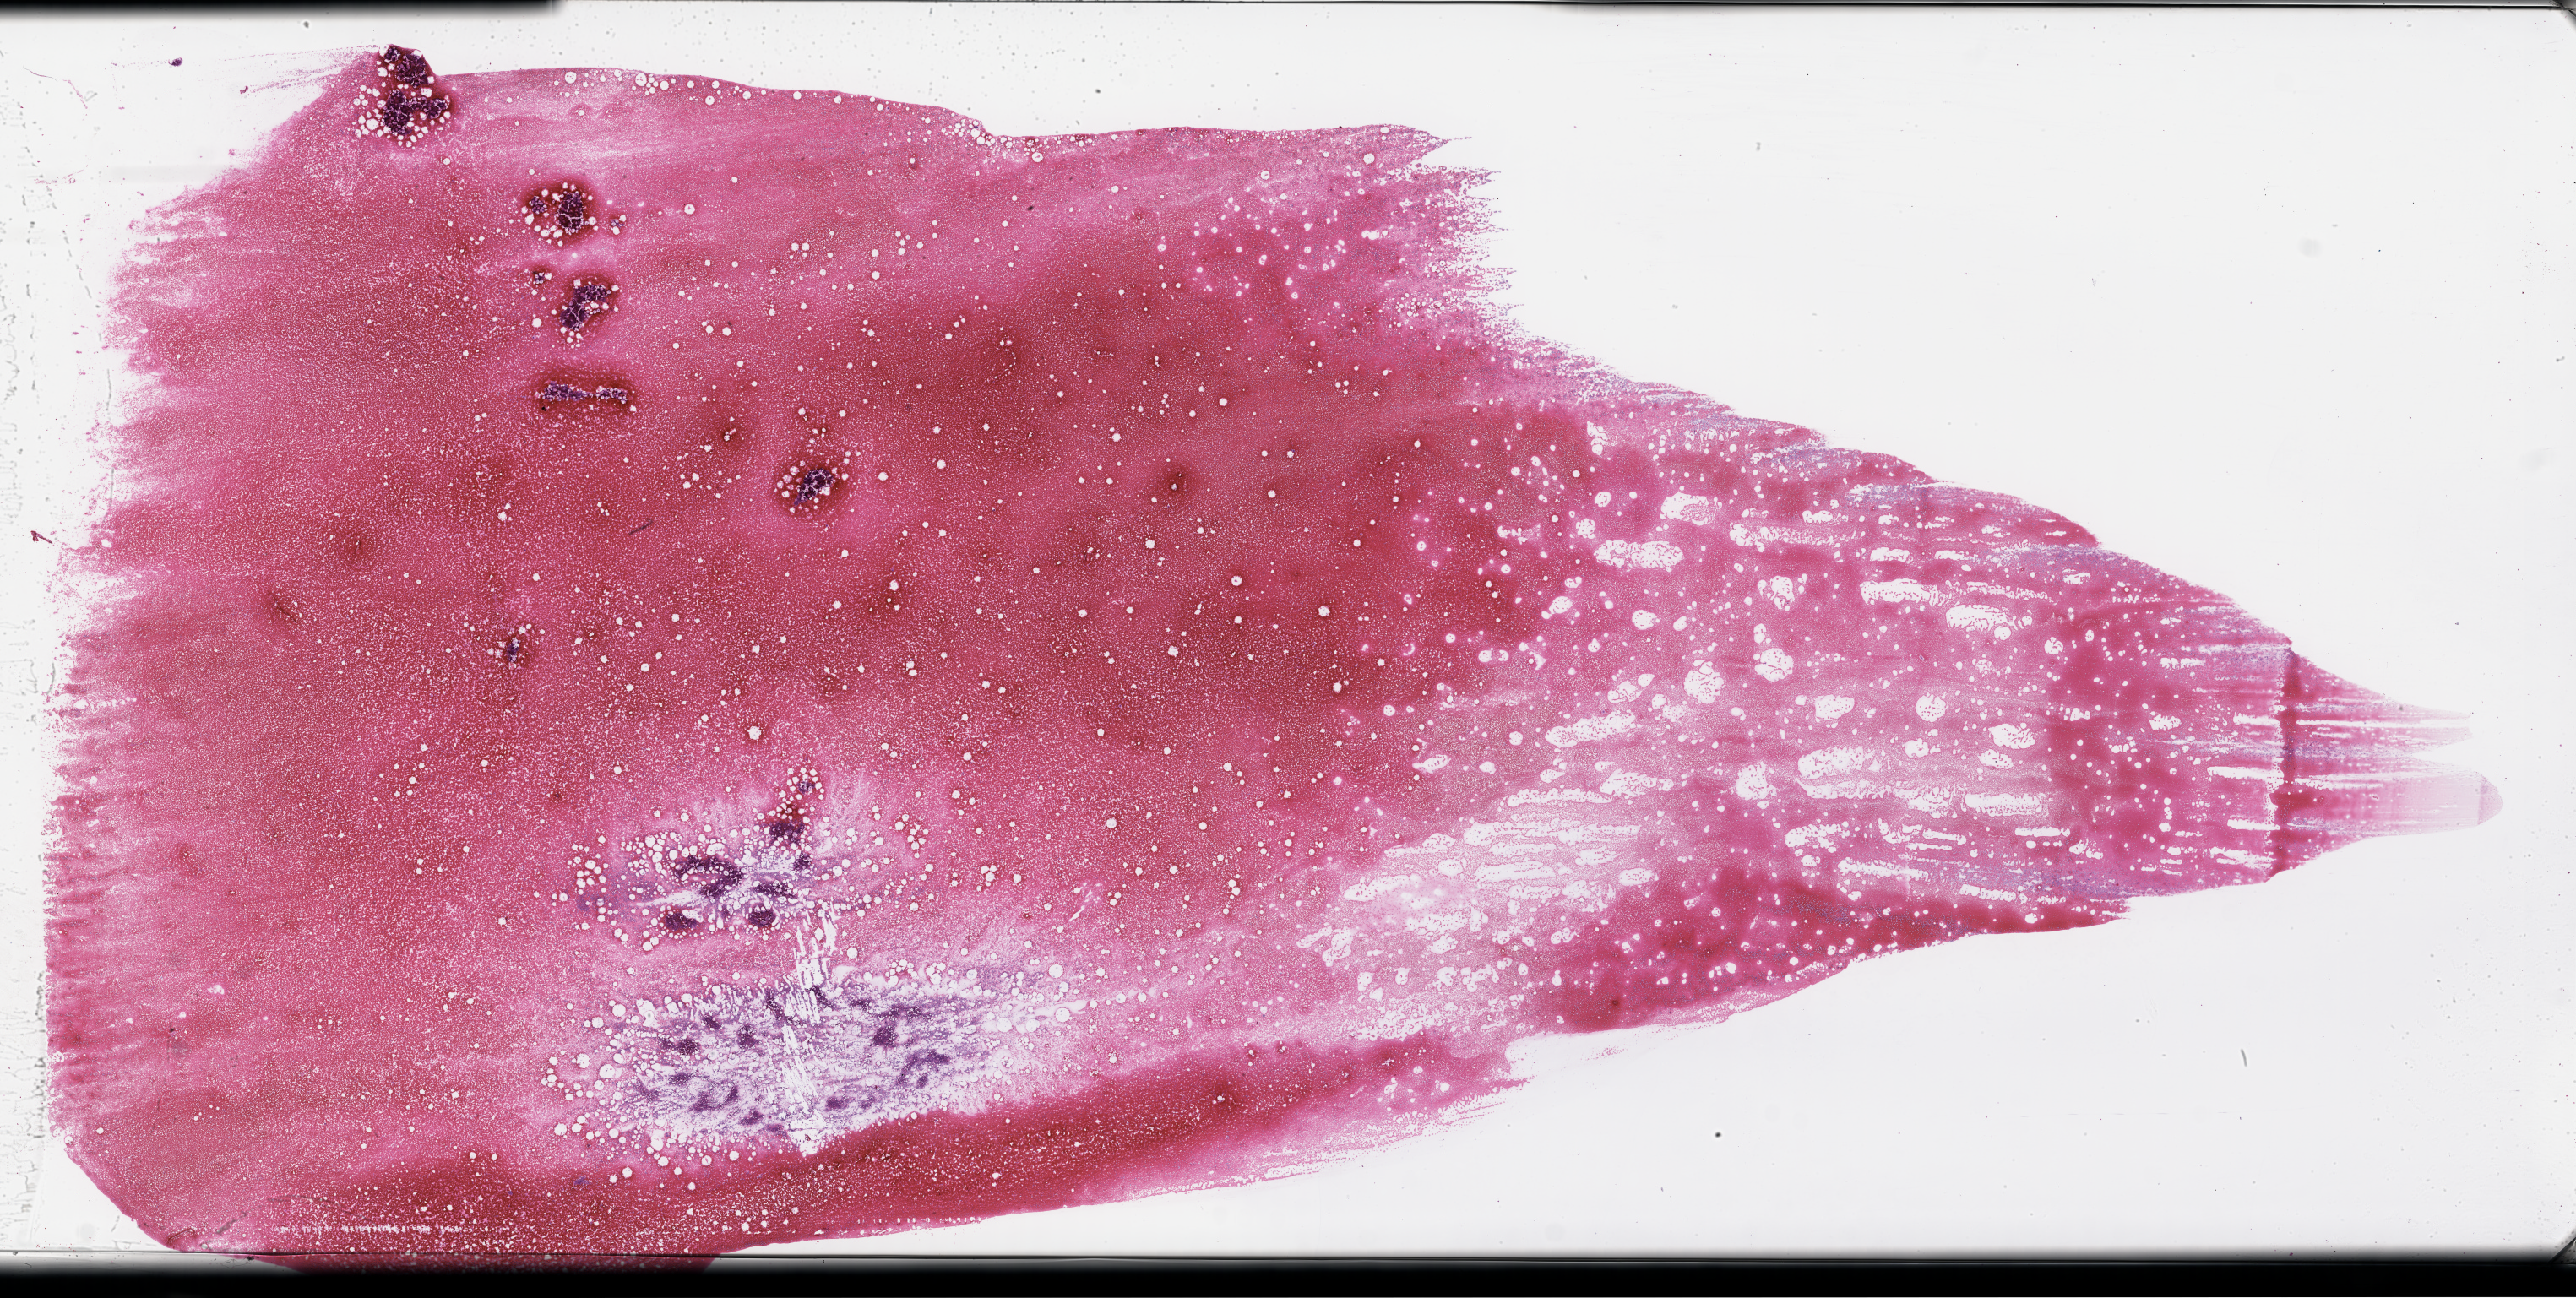
Hematoxylin and eosin (H&E) whole-slide image, whole scanned area (about 49.3 x 24.8 mm) shown as a low-resolution overview; paraffin-embedded section (EDTA recorded as fixative); tissue site: bone marrow; archival tissue. Patient: female.
* this section: primary tumour tissue
* diagnosis: Plasma Cell Myeloma